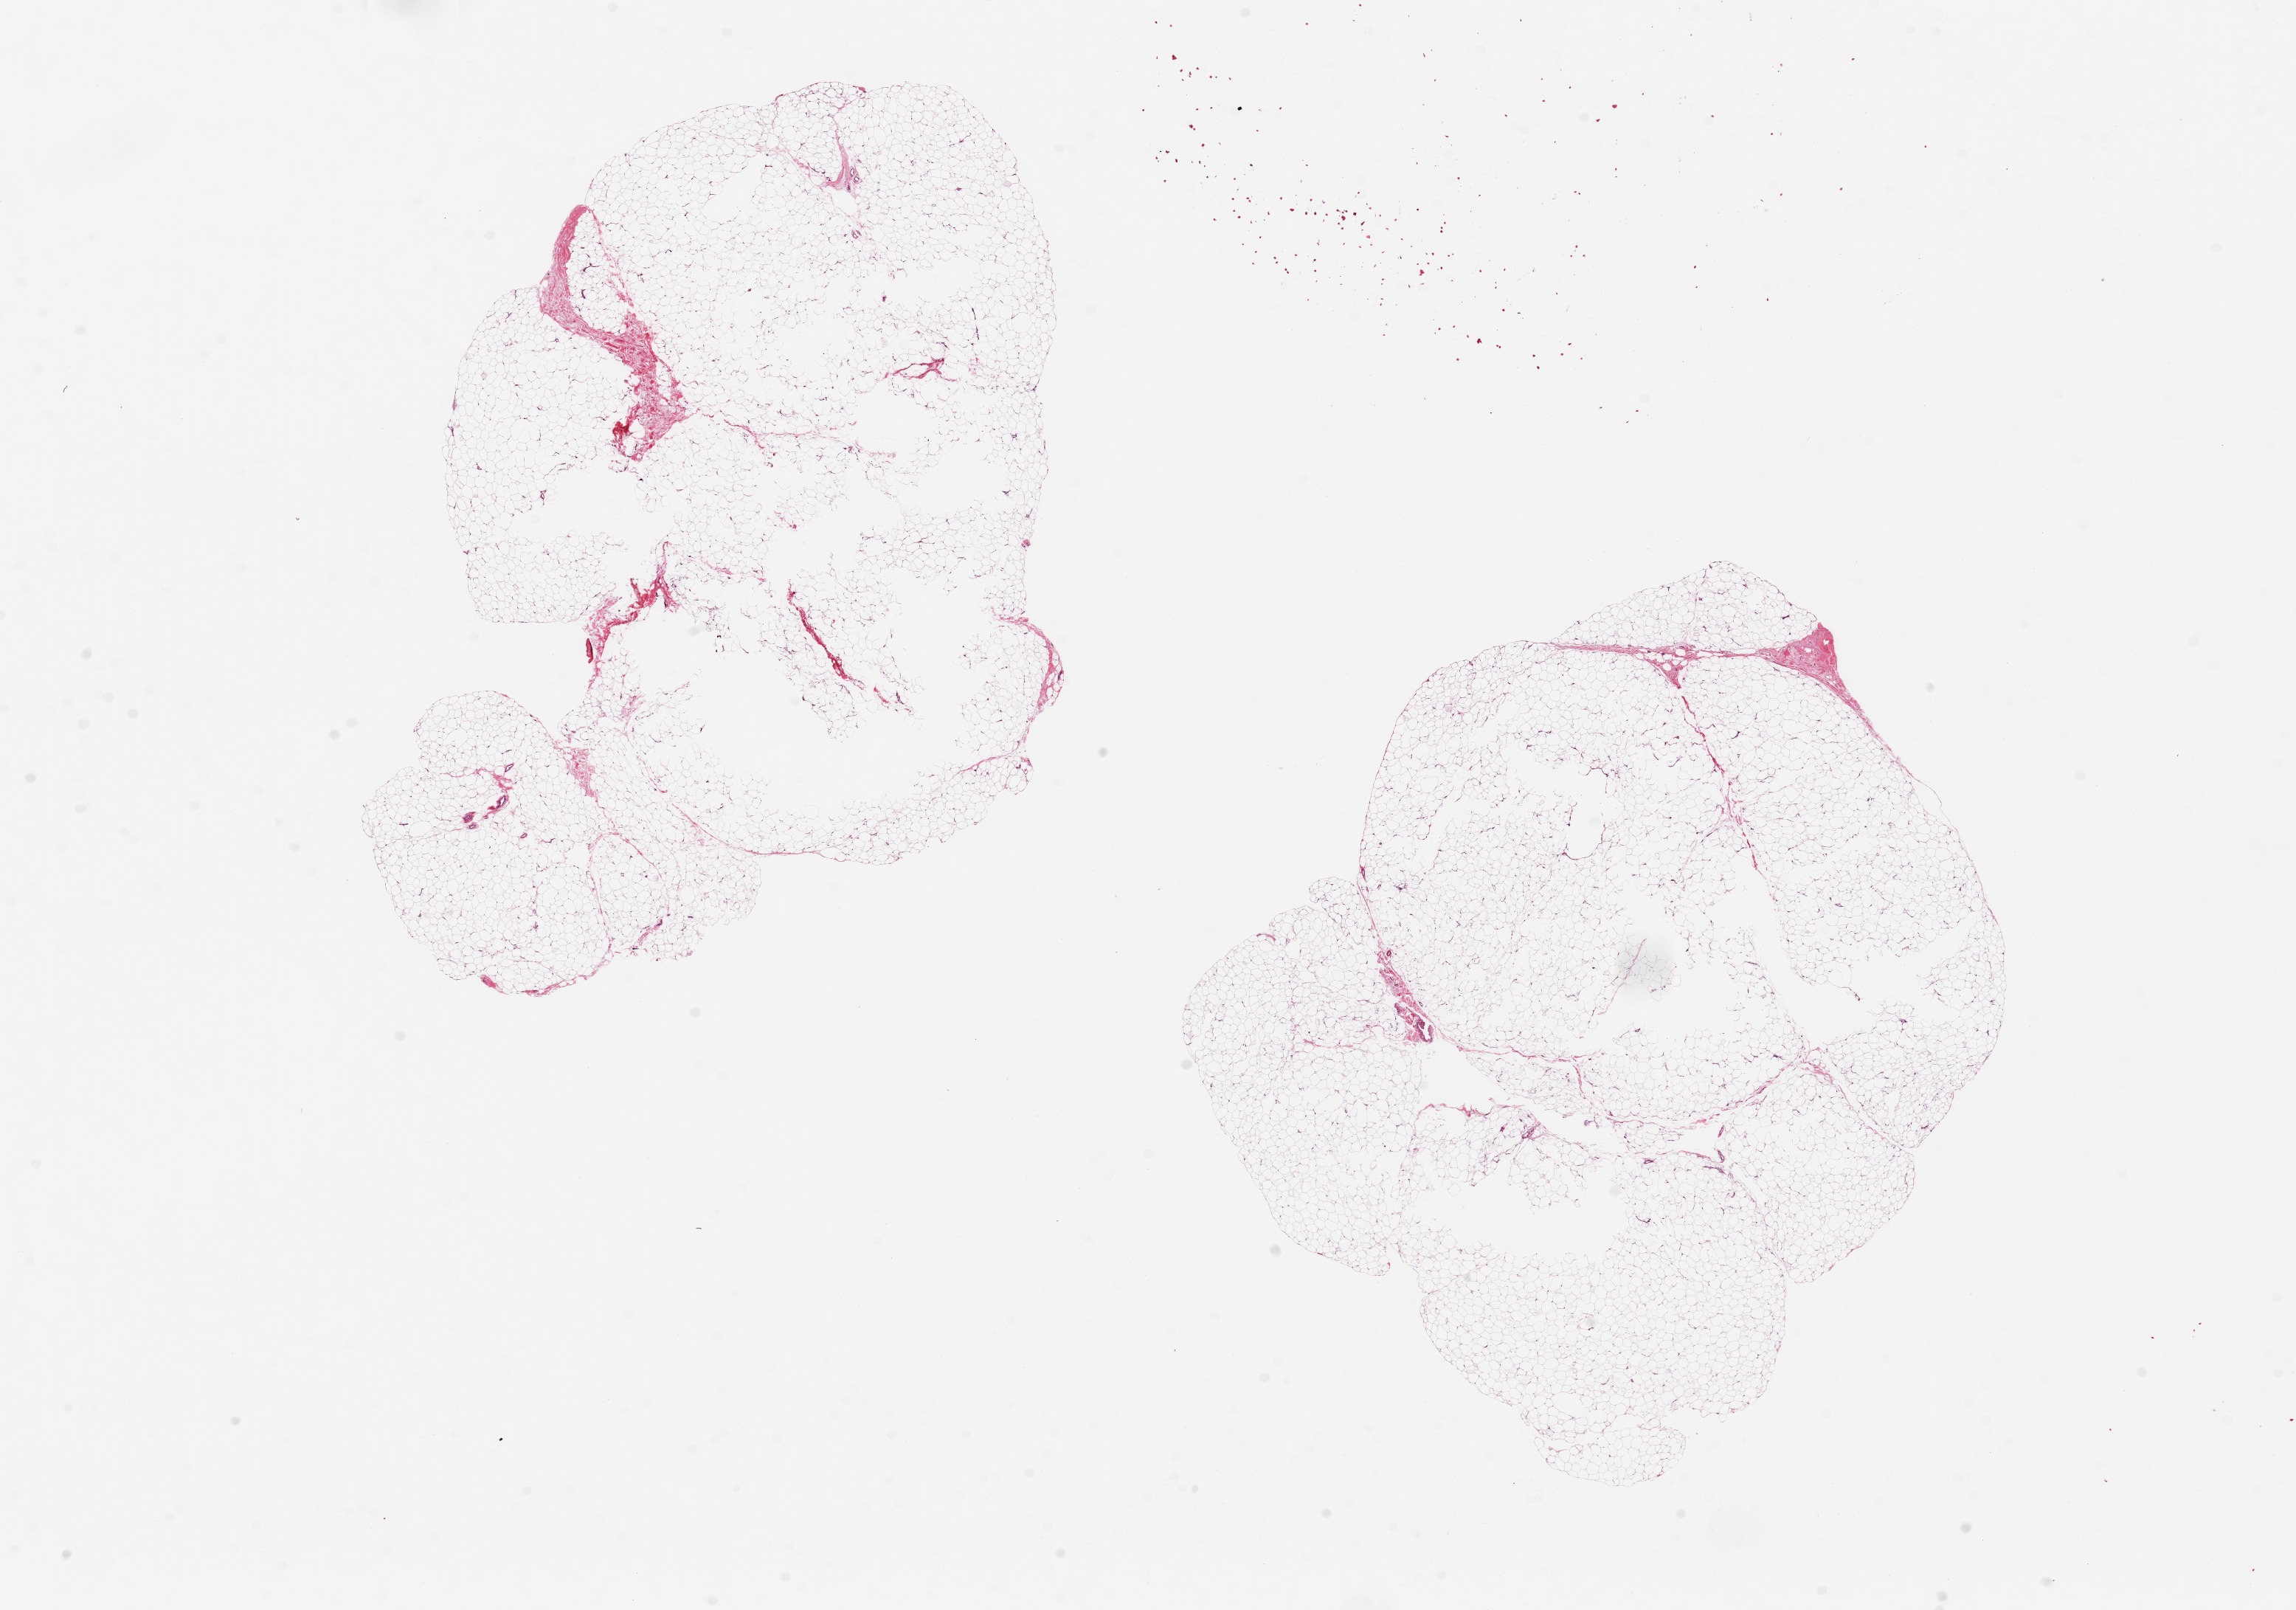
Whole-slide image, hematoxylin and eosin (H&E) stain — shown as a low-resolution overview of the whole scanned area (about 24.6 x 17.3 mm), PAXgene-fixed paraffin-embedded (PFPE) section, target tissue: adipose tissue, donor tissue sample. Donor sex: female.
* reviewer comment on this tissue sample: 2 pieces, 8x8 & 8x7.5mm; small hollow artifacts, not centrally unfixed